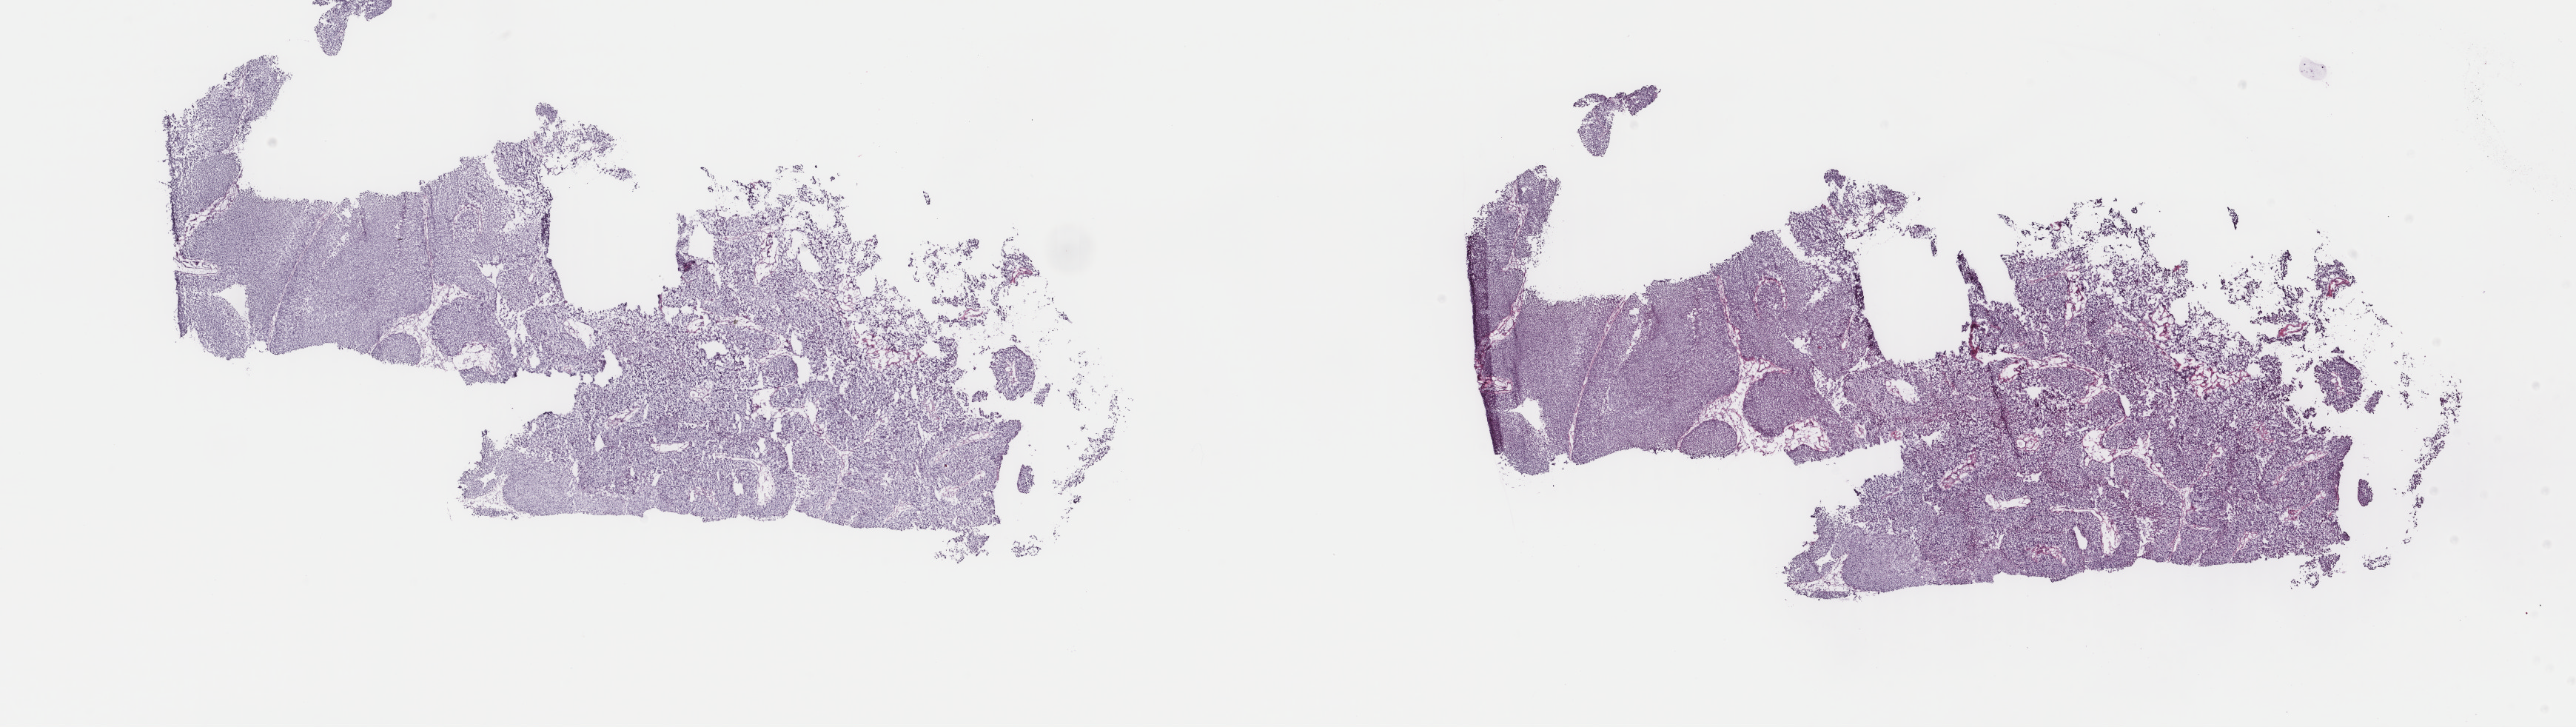
Digitized H&E-stained tissue section (whole slide), whole scanned area (about 27.6 x 7.8 mm) shown as a low-resolution overview, frozen section, primary tumour sample from the bladder. Male, age 48 years at initial diagnosis. Histologic grade: low grade. Slide review estimates, as recorded: tumour cells 90%, tumour nuclei 90%, normal cells 0%, stromal cells 9%, necrosis 1%. Inflammatory infiltration, as recorded: lymphocyte infiltration 2%, monocyte infiltration 1%, neutrophil infiltration 1%.
- diagnosis: Papillary transitional cell carcinoma
- AJCC pathologic stage: II (7th edition)